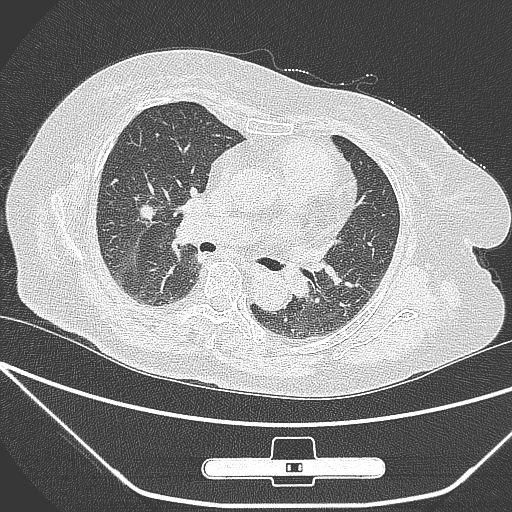
Chest CT, one axial slice; lung window (W 1500 / L -600 HU); 512 × 512 image matrix. Female patient, age 65 years. Case-level facts recorded for this patient, not image findings: clinical TNM (as recorded): T1c N0 M0.
Outlined on this slice (bounding box drawn by a radiologist):
- lung tumour (recorded histology: adenocarcinoma): bounding box (x1, y1, x2, y2) in pixels: (134, 200, 154, 228)